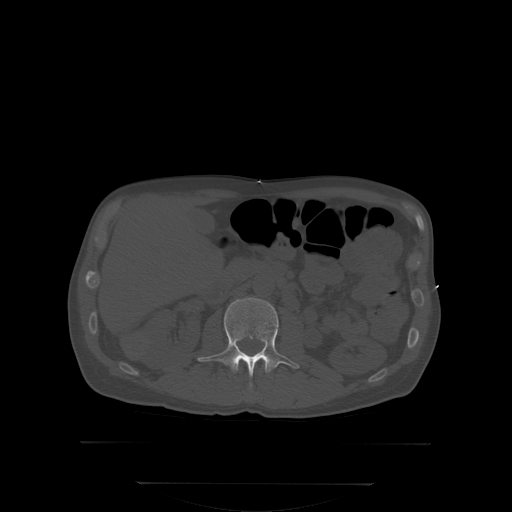
CT including the spine, one axial slice; slice 139 of 350 in the series (ordered by position); bone window (W 1800 / L 400 HU); 2.5 mm slice thickness; 512 × 512 image matrix, field of view 500 × 500 mm. Patient: male, 58 years. From the clinical record (not read from this slice): primary cancer: prostate; vertebrae with lytic lesions (as recorded): L1.
Annotated regions visible in this slice (semi-automatic segmentation, software-assisted and operator-edited):
- L2 vertebra: bounding box <197,297,300,390> (left, top, right, bottom; pixels)